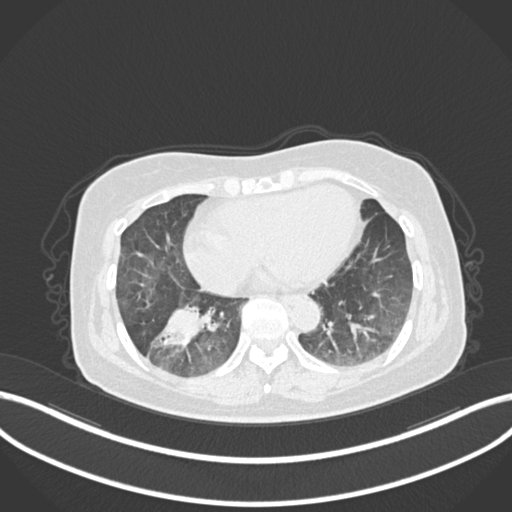
Chest CT, one axial slice; slice 44 of 222 in the series (ordered by position); reconstruction kernel B30f; lung window (W 1500 / L -600 HU); 1 mm slice thickness; 512 × 512 image matrix, field of view 400 × 400 mm. Patient: female, 67 years. Case-level facts recorded for this patient, not image findings: clinical TNM (as recorded): T1c N1 M0; histopathological grade: G2-3.
Outlined on this slice (rectangle marked by the reading radiologist):
- lung tumour (recorded histology: adenocarcinoma): bounding box (x1, y1, x2, y2) in pixels: (151, 296, 214, 353)